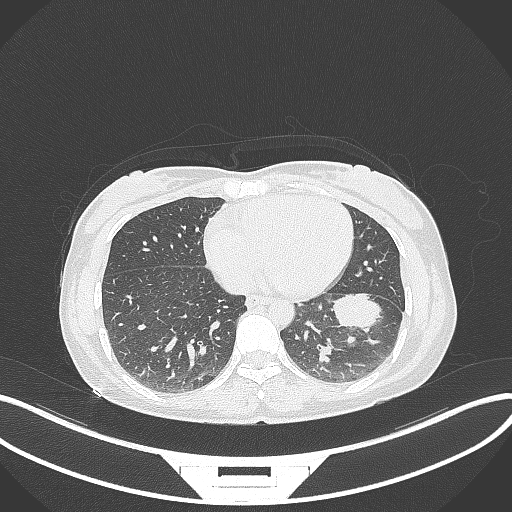
Chest CT, one axial slice. Position 13 of 244 along the scan axis. 120 kVp. Lung window (W 1500 / L -600 HU). 1 mm slice thickness. 512 × 512 image matrix. Female patient, age 41 years. Case-level facts recorded for this patient, not image findings: clinical TNM (as recorded): T2a N3 M1b.
Outlined on this slice (rectangle marked by the reading radiologist):
- lung tumour (recorded histology: adenocarcinoma): bounding box [x1, y1, x2, y2] px = [333, 290, 383, 332]